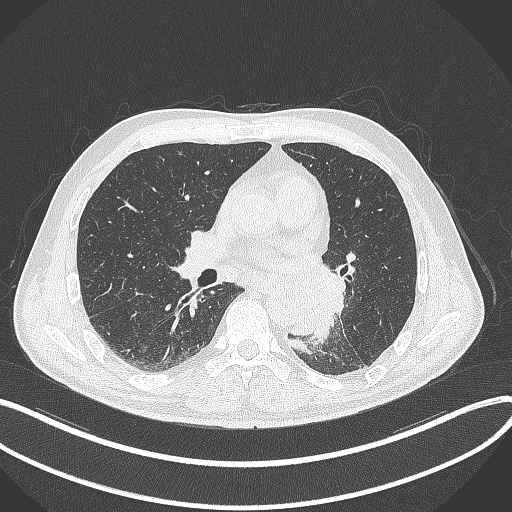
Chest CT, one axial slice. Position 170 of 329 along the scan axis. 120 kVp. Lung window (W 1500 / L -600 HU). 512 × 512 image matrix, field of view 400 × 400 mm. Male patient, age 59 years. Case-level facts recorded for this patient, not image findings: clinical TNM (as recorded): T2a N2 M0.
Outlined on this slice (bounding box drawn by a radiologist):
- lung tumour (recorded histology: squamous cell carcinoma): box from (x=287, y=259) to (x=346, y=342) px